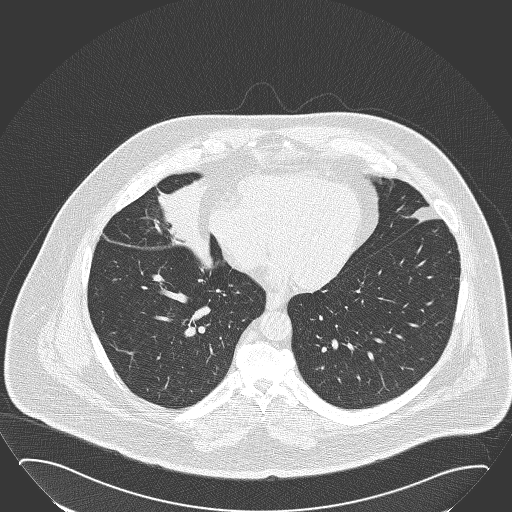
Low-dose screening chest CT, one axial slice; position 63 of 168 along the scan axis; lung window (W 1500 / L -600 HU); 2 mm slice thickness; 512 × 512 image matrix, field of view 432 × 432 mm.
Structures marked on this image (expert manual segmentation):
- lesion 1 (tumor, hilum of right lung): bounding box [x1, y1, x2, y2] px = [158, 178, 213, 272]